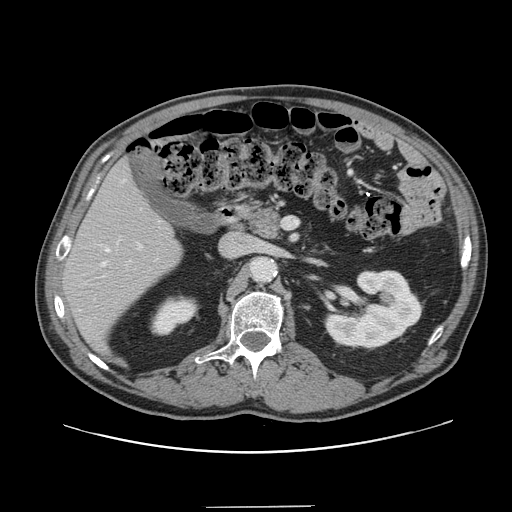
Contrast-enhanced abdominal CT, one axial slice. Slice 73 of 139 in the series (ordered by position). Intravenous contrast given. Soft-tissue window (W 400 / L 40 HU). 2.5 mm slice thickness. 512 × 512 image matrix, field of view 397 × 397 mm. Male patient, age 64 years. From the clinical record (not read from this slice): diagnosis: colorectal cancer liver metastases, imaged before liver resection; multiple liver metastases: yes.
Outlined on this slice (expert manual segmentation):
- hepatic veins: bounding box [x1, y1, x2, y2] px = [101, 180, 131, 267]
- liver: [64, 163, 181, 349]
- planned liver remnant (the part of the liver to remain after resection): [64, 163, 182, 349]
- portal vein (with intrahepatic branches): [138, 243, 142, 250]